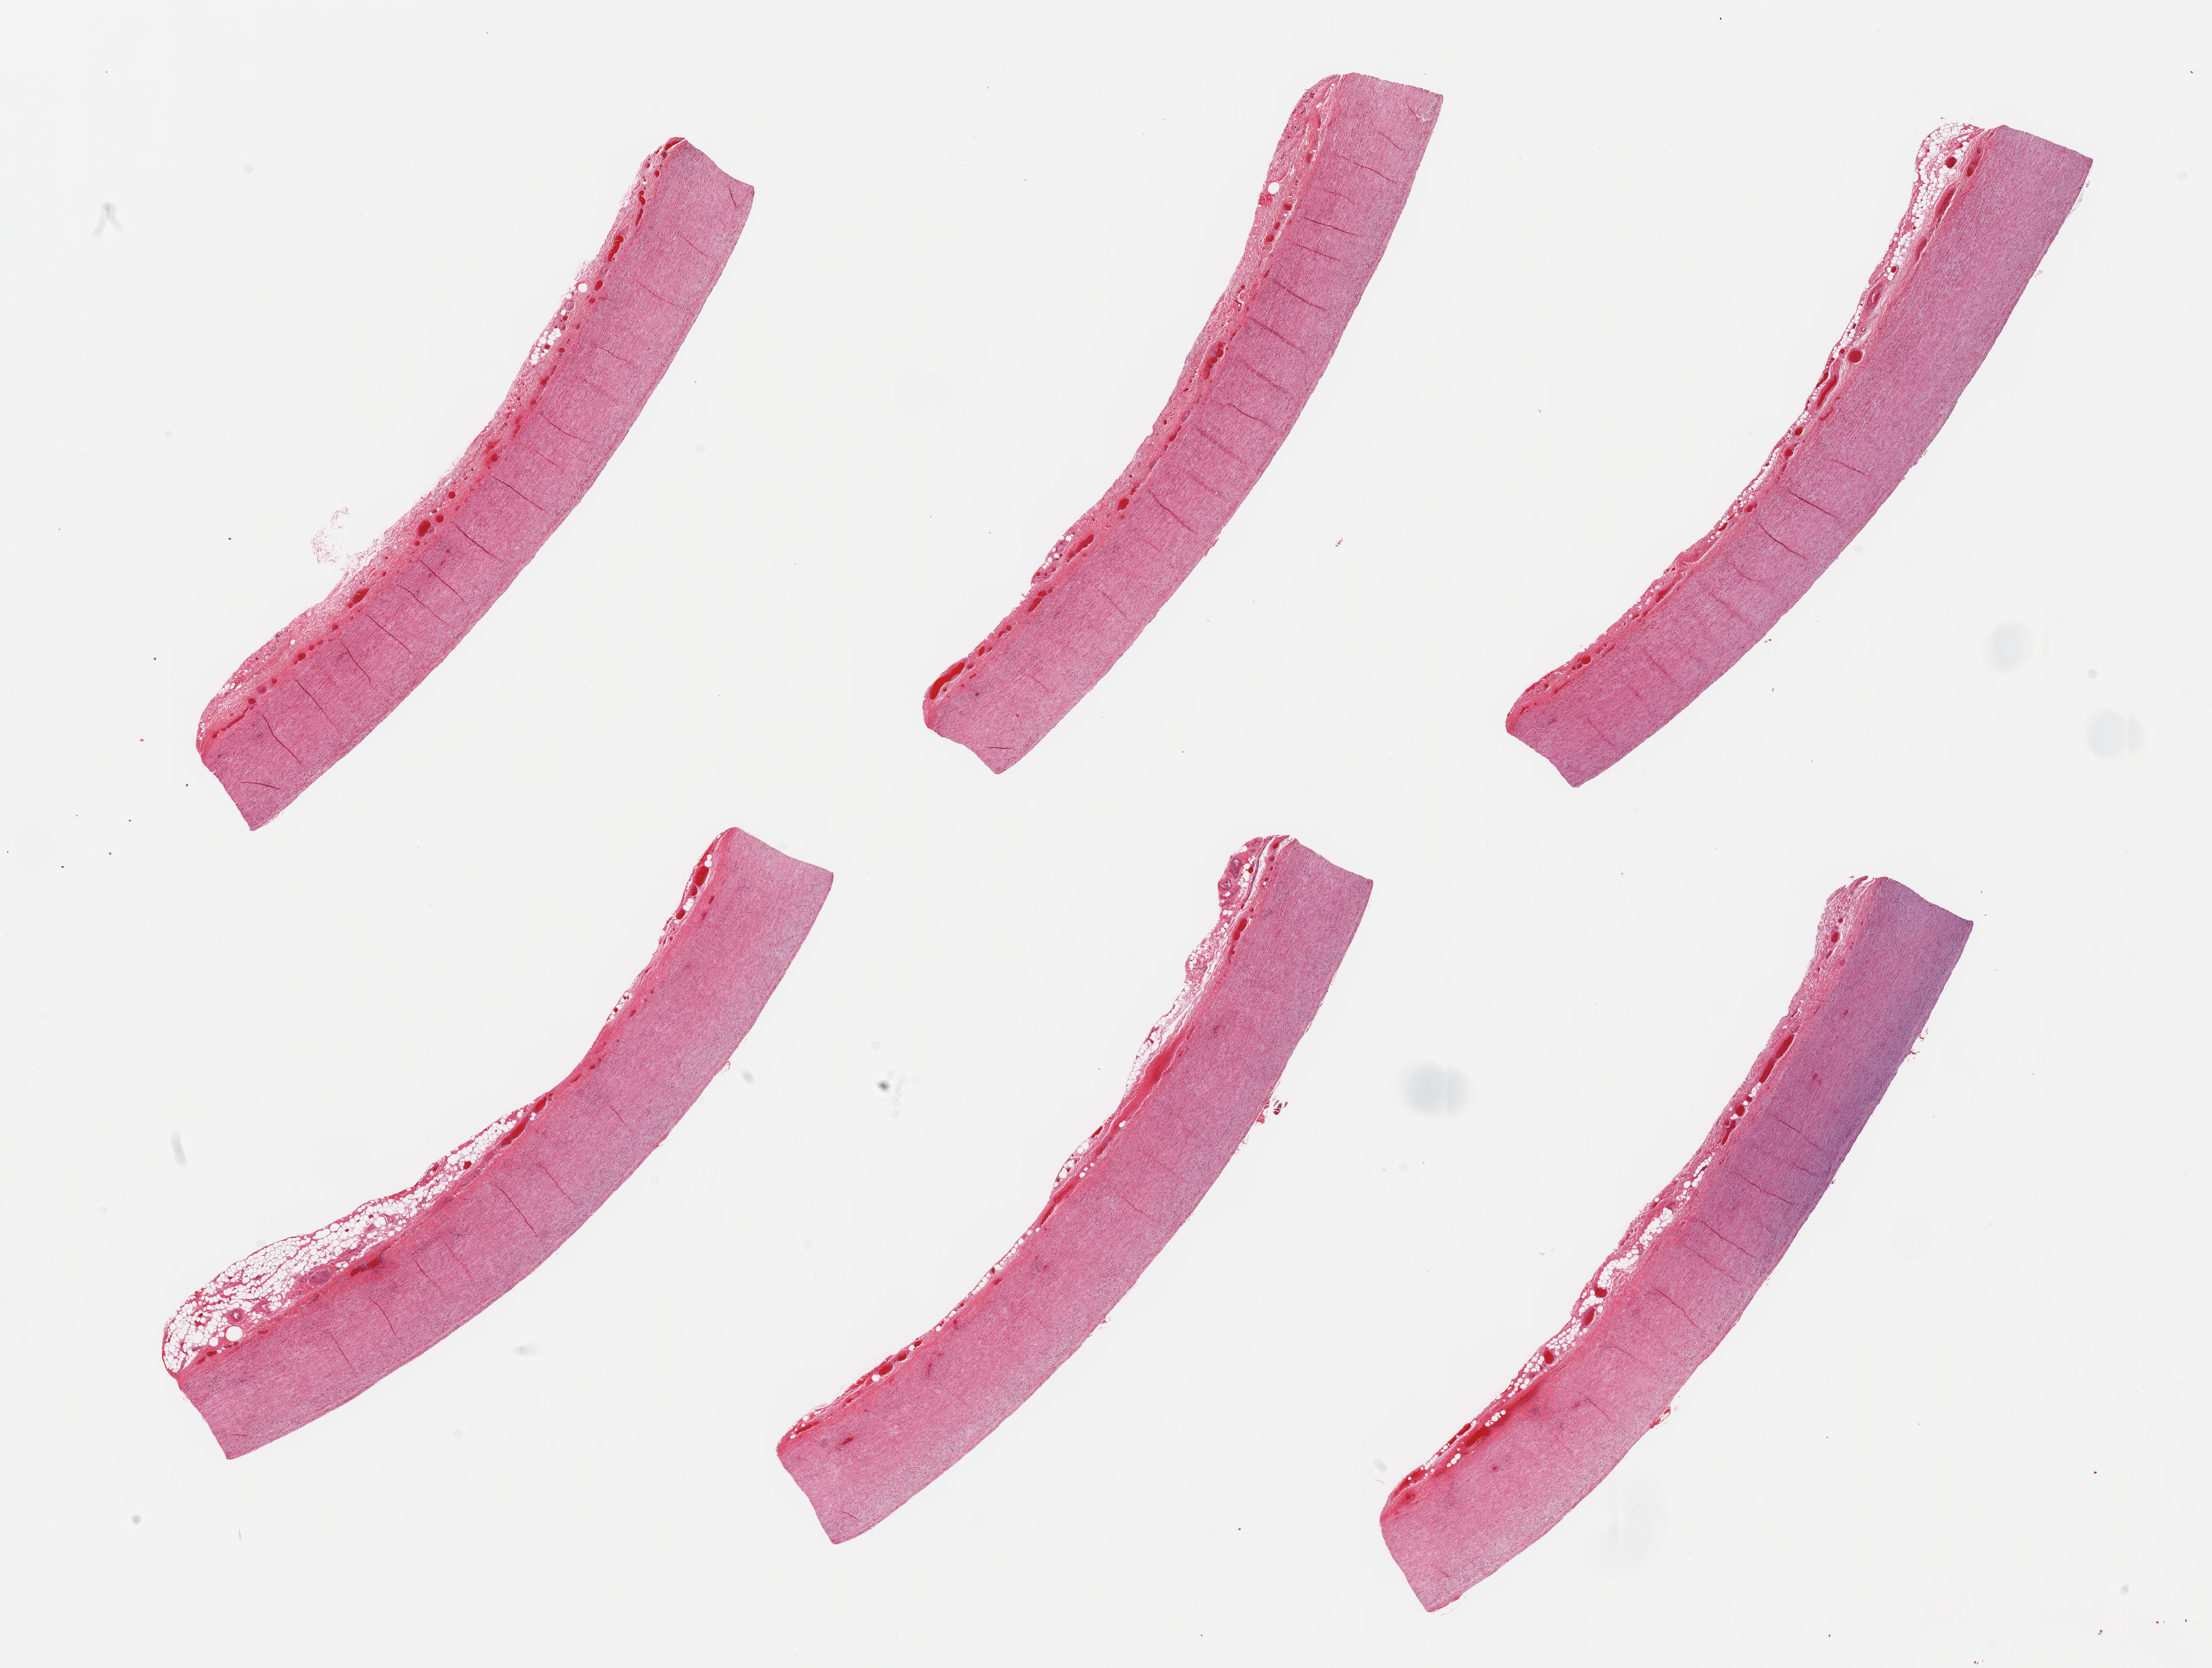
Digitized haematoxylin and eosin-stained section — a low-resolution overview of the entire scanned area, about 25.6 x 19.3 mm. PAXgene-fixed, paraffin-embedded tissue. Sampled site (target tissue): aorta. Tissue donor sample. Donor: male.
• review note (as recorded): 6 pieces; well trimmed, no lesions